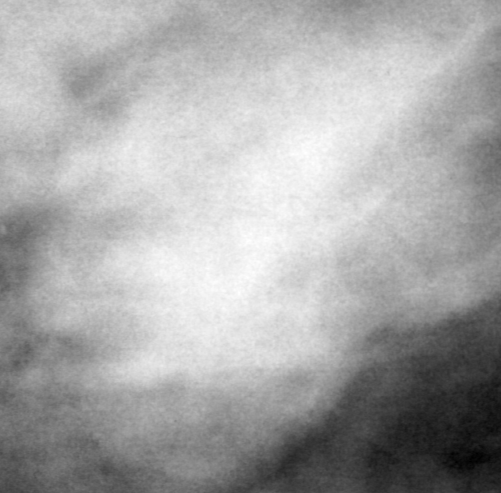
Cropped region of a digitized screen-film mammogram centred on a radiologist-marked abnormality, left breast, MLO view.
Marked abnormality: mass, shape lobulated, margins obscured; BI-RADS assessment category 4; pathology result (as recorded, not read from the image): benign.